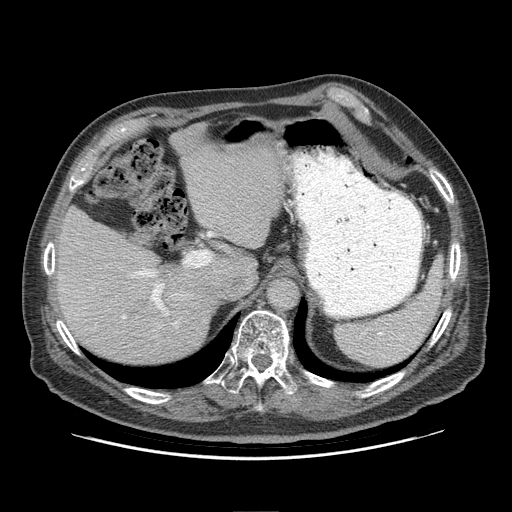
Contrast-enhanced abdominal CT (liver protocol), one axial slice; position 64 of 95 along the scan axis; soft-tissue window (W 400 / L 40 HU); 2.5 mm slice thickness; 512 × 512 image matrix, field of view 400 × 400 mm. From the clinical record (not read from this slice): diagnosis: hepatocellular carcinoma (patient treated with transarterial chemoembolisation; whether this scan precedes or follows treatment is not stated here); TNM stage (as recorded): Stage-IVB; Child-Pugh class: A; tumour differentiation: well differentiated.
Annotated regions visible in this slice (semi-automatically segmented with operator editing):
- abdominal aorta: bounding box (x1, y1, x2, y2) in pixels: (268, 278, 298, 310)
- liver parenchyma outside the tumour (the mass and vessels are separate outlines, so this box may not span the whole liver): (56, 122, 288, 362)
- liver vessels: (122, 269, 176, 323)